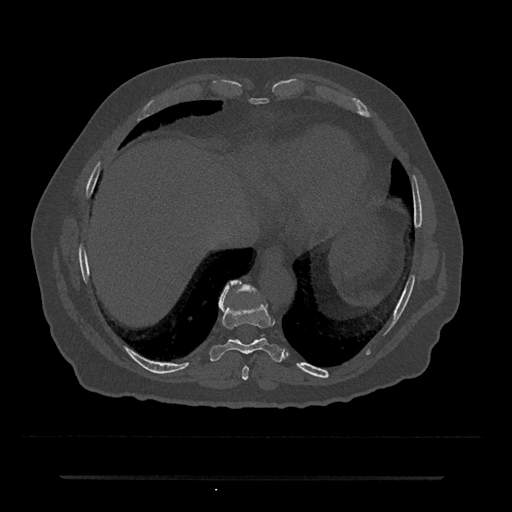
CT including the spine, one axial slice; reconstruction kernel Br40s/3; 120 kVp; bone window (W 1800 / L 400 HU); 512 × 512 image matrix, field of view 437 × 437 mm. Male patient, age 69 years. Case-level facts recorded for this patient, not image findings: primary cancer: prostate.
Structures marked on this image (semi-automatic segmentation, software-assisted and operator-edited):
- T10 vertebra: bounding box <236,281,257,292> (left, top, right, bottom; pixels)
- T8 vertebra: <242,366,249,380>
- T9 vertebra: <209,281,285,362>